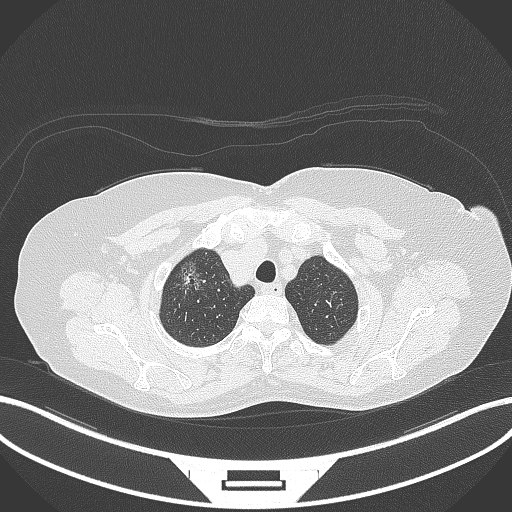
Chest CT, one axial slice; position 306 of 365 along the scan axis; lung window (W 1500 / L -600 HU); 1 mm slice thickness; 512 × 512 image matrix, field of view 400 × 400 mm. Female patient, age 62 years. From the clinical record (not read from this slice): clinical TNM (as recorded): T1c N0 M0.
Structures marked on this image (rectangle marked by the reading radiologist):
- lung tumour (recorded histology: adenocarcinoma): bounding box [x1, y1, x2, y2] px = [173, 256, 211, 300]